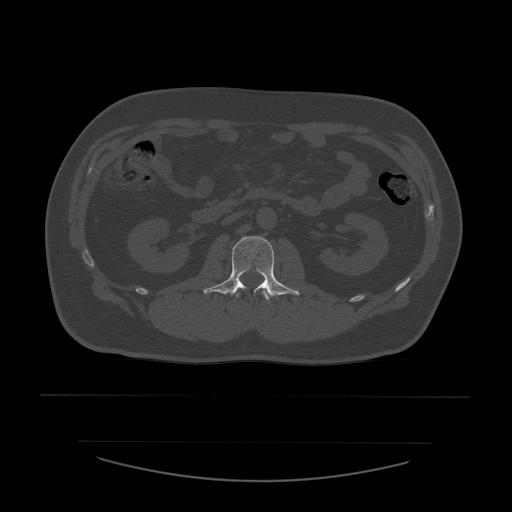
CT including the spine, one axial slice. Slice 204 of 532 in the series (ordered by position). 120 kVp. Bone window (W 1800 / L 400 HU). 1.25 mm slice thickness. 512 × 512 image matrix, field of view 441 × 441 mm. Patient age 44 years. From the clinical record (not read from this slice): primary cancer: soft tissue sarcoma.
Structures marked on this image (semi-automatically segmented with operator editing):
- L1 vertebra: bounding box [x1, y1, x2, y2] px = [235, 291, 270, 301]
- L2 vertebra: [204, 237, 300, 299]